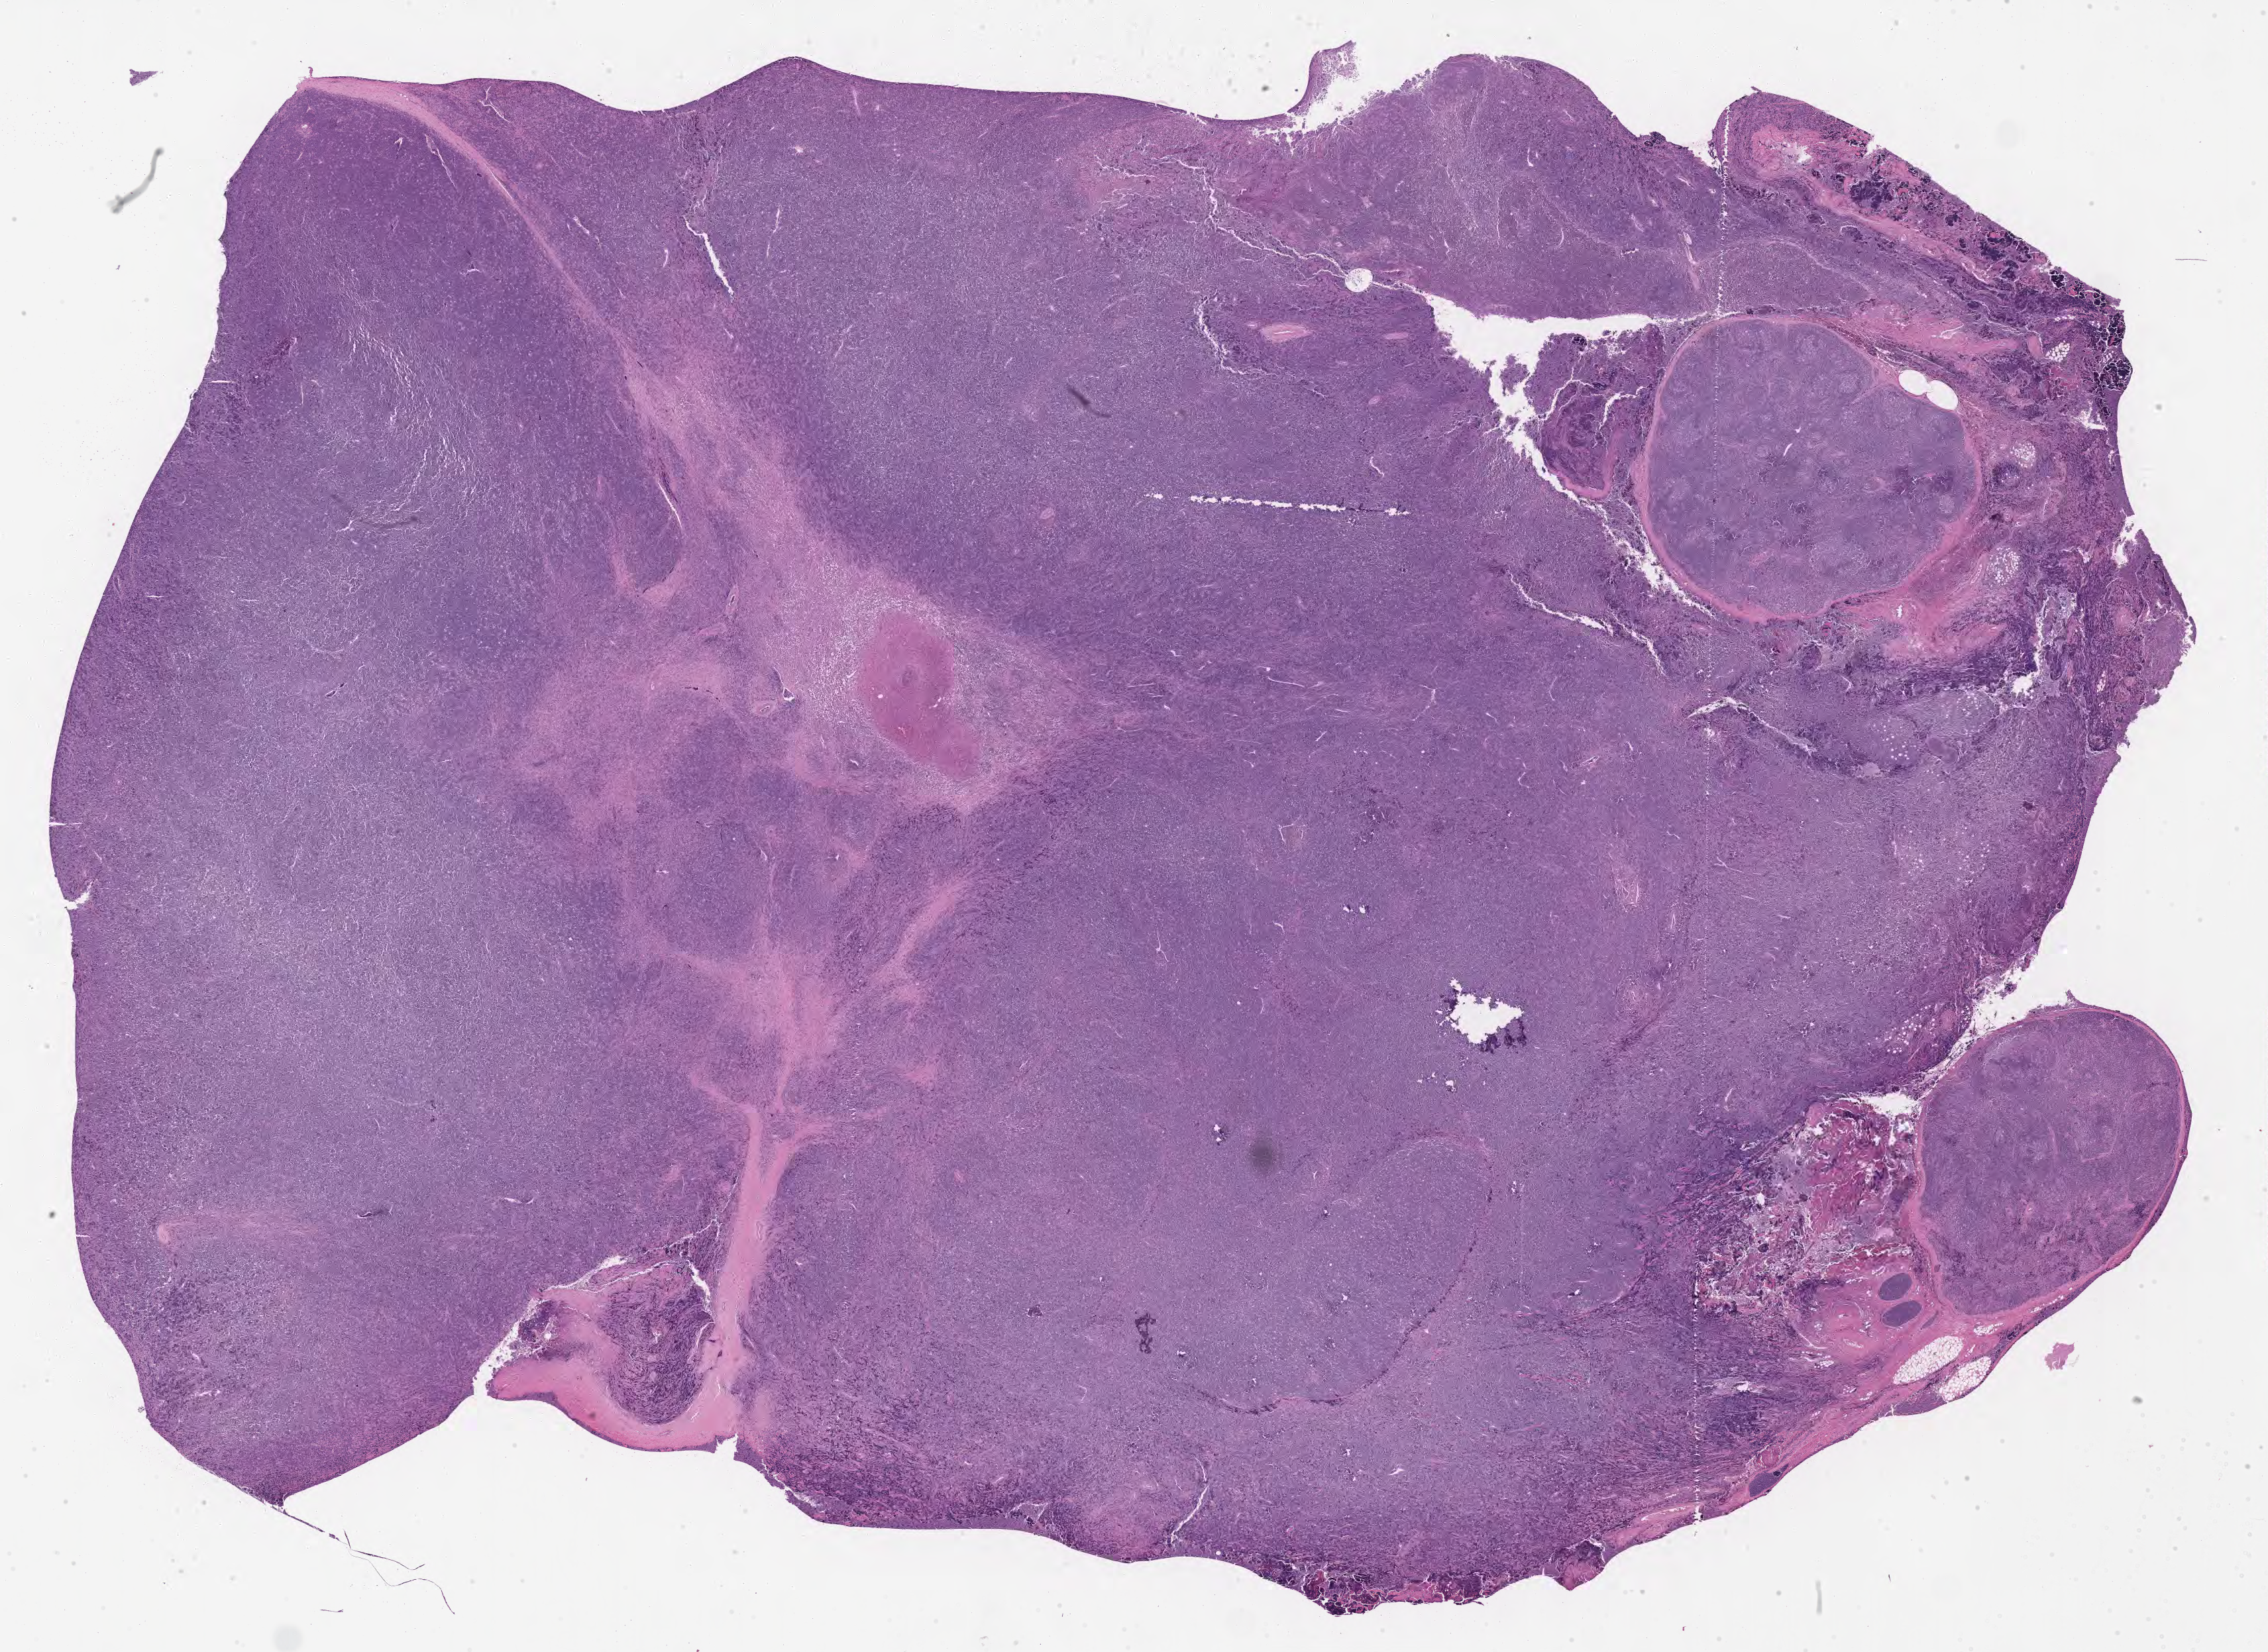
Whole-slide image, hematoxylin and eosin (H&E) stain, whole scanned area (about 27.7 x 20.2 mm) shown as a low-resolution overview. Tumor tissue. Anatomic site: lymph node of head and neck. Male patient; age at initial diagnosis 3 years.
Histologic diagnosis: Burkitt lymphoma, NOS.